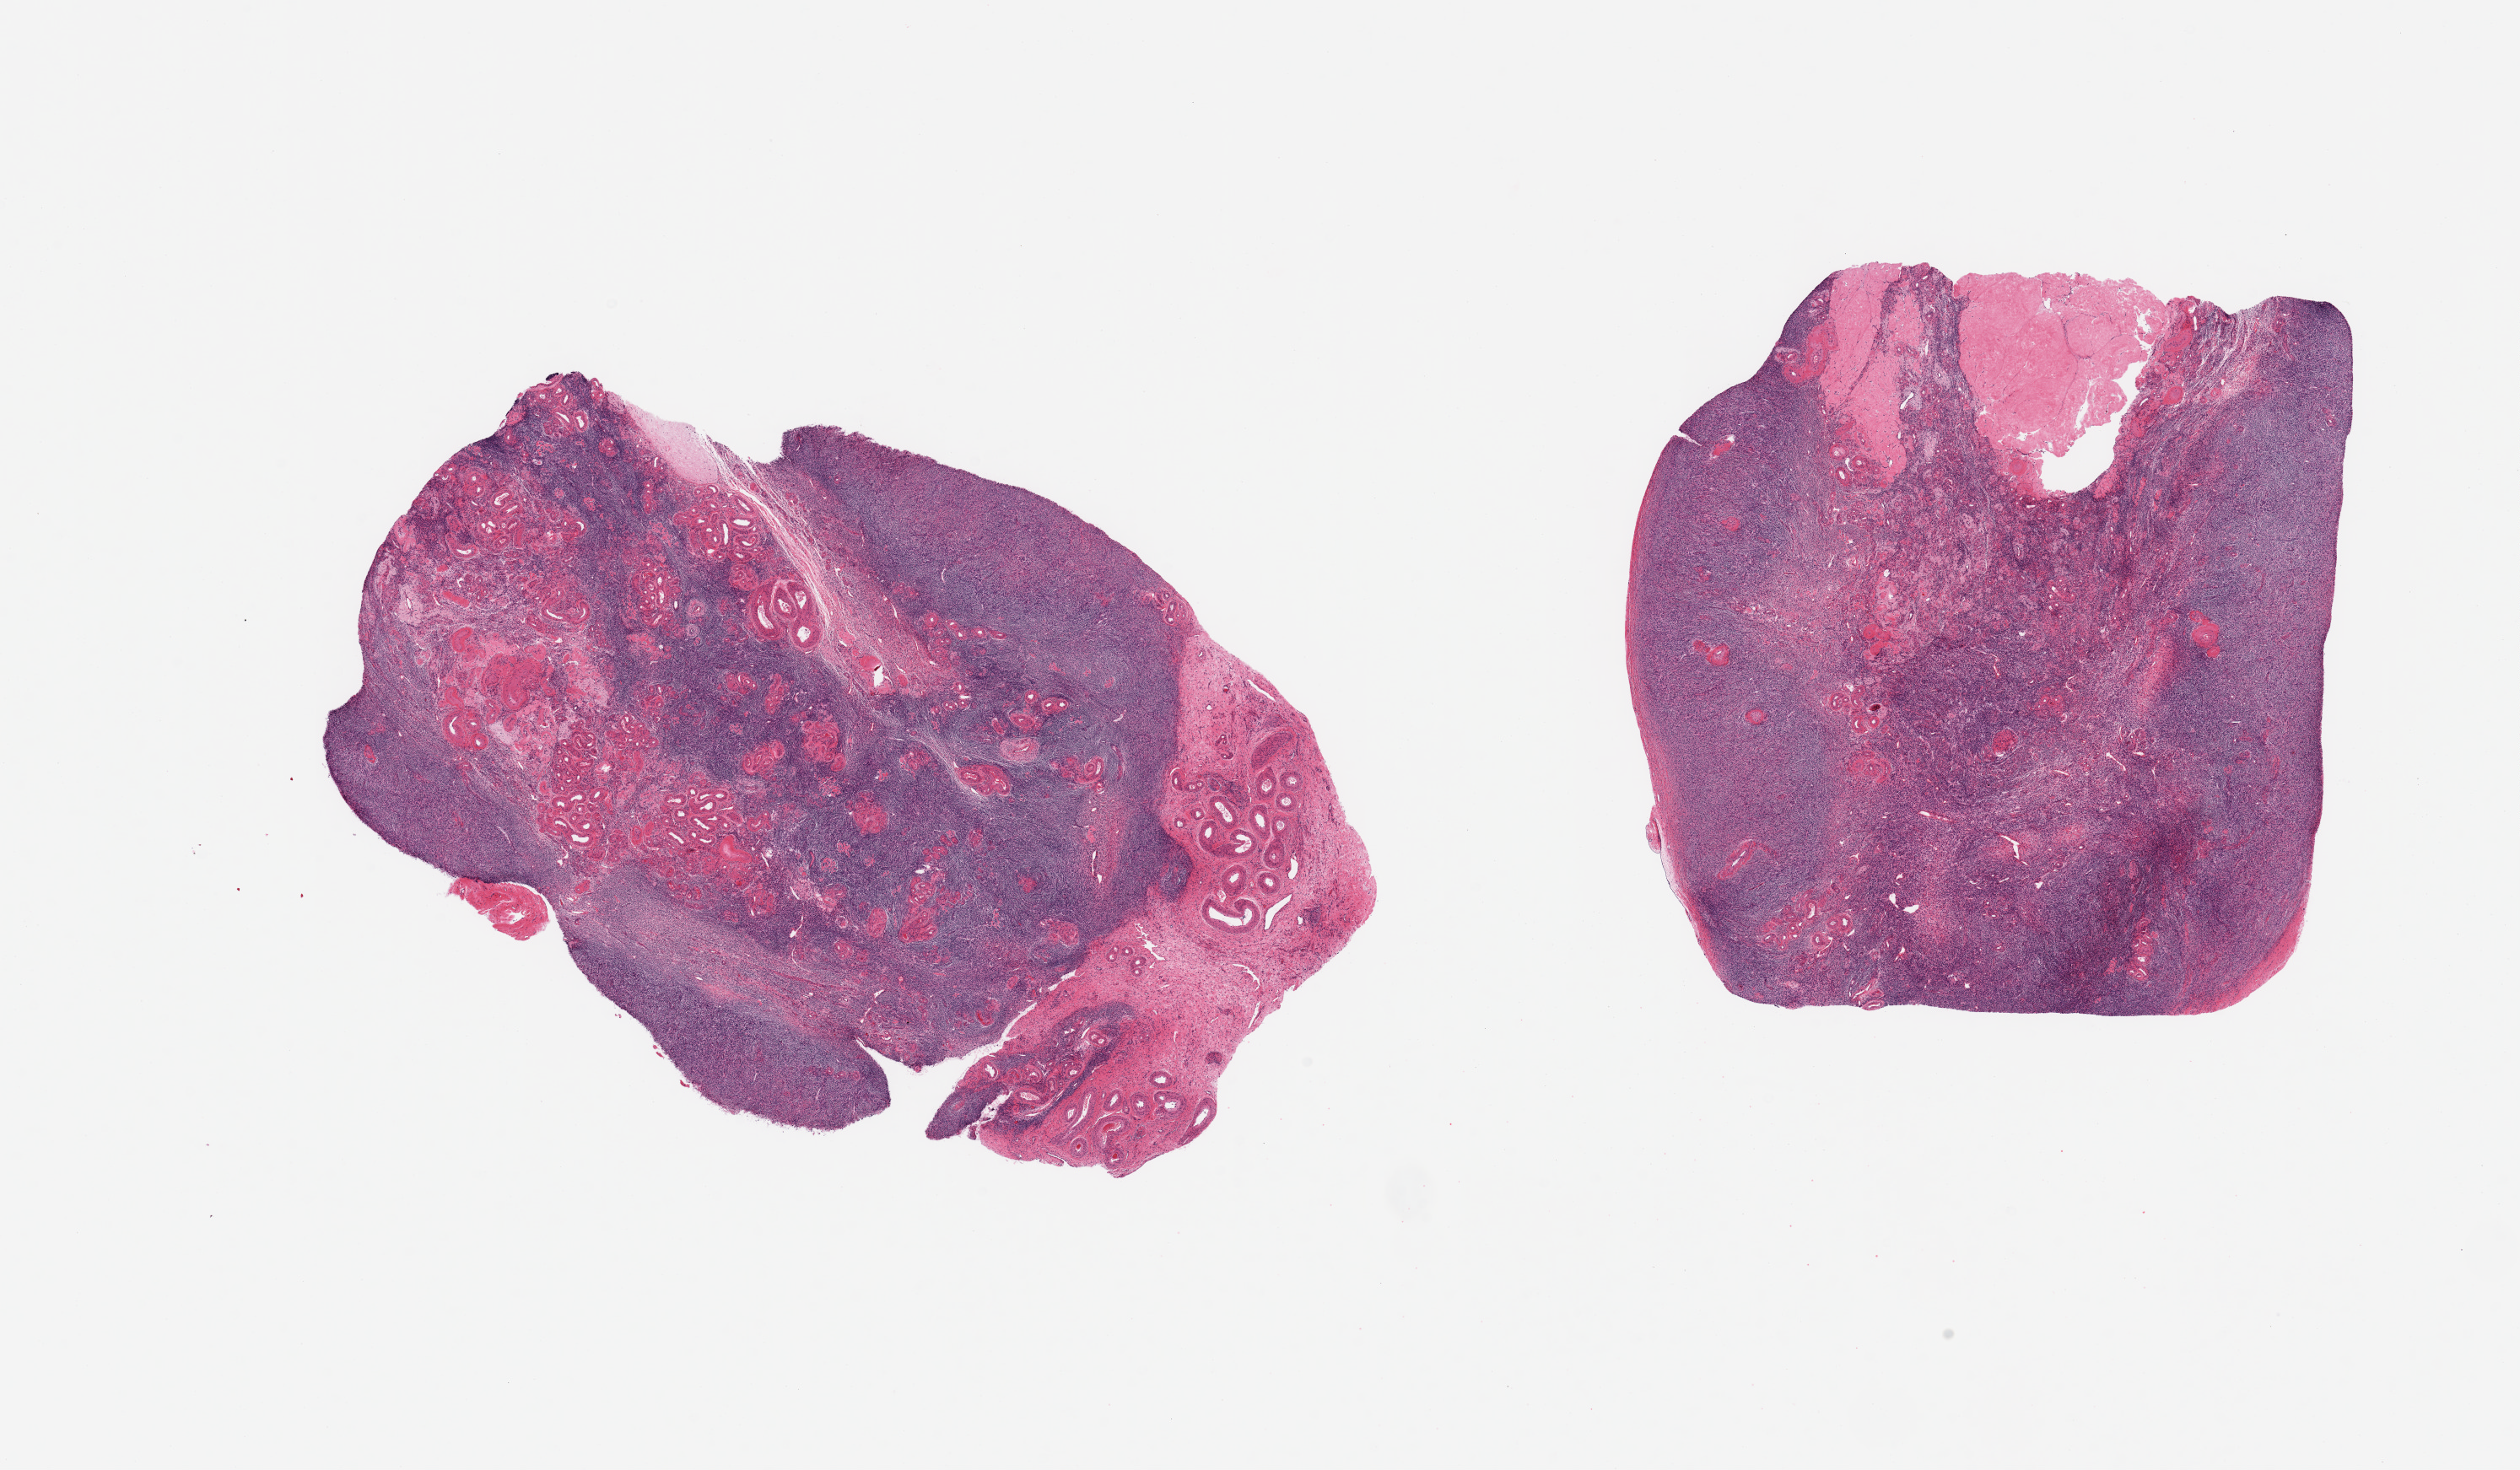
Whole-slide image, H&E stain — a low-resolution overview of the entire scanned area, about 23.6 x 13.8 mm. PAXgene-fixed paraffin-embedded (PFPE) section. Target tissue: ovary. Donor tissue sample. Donor: female.
Reviewer comment on this tissue sample: 2 pieces, normal post menopausal regressive changes.